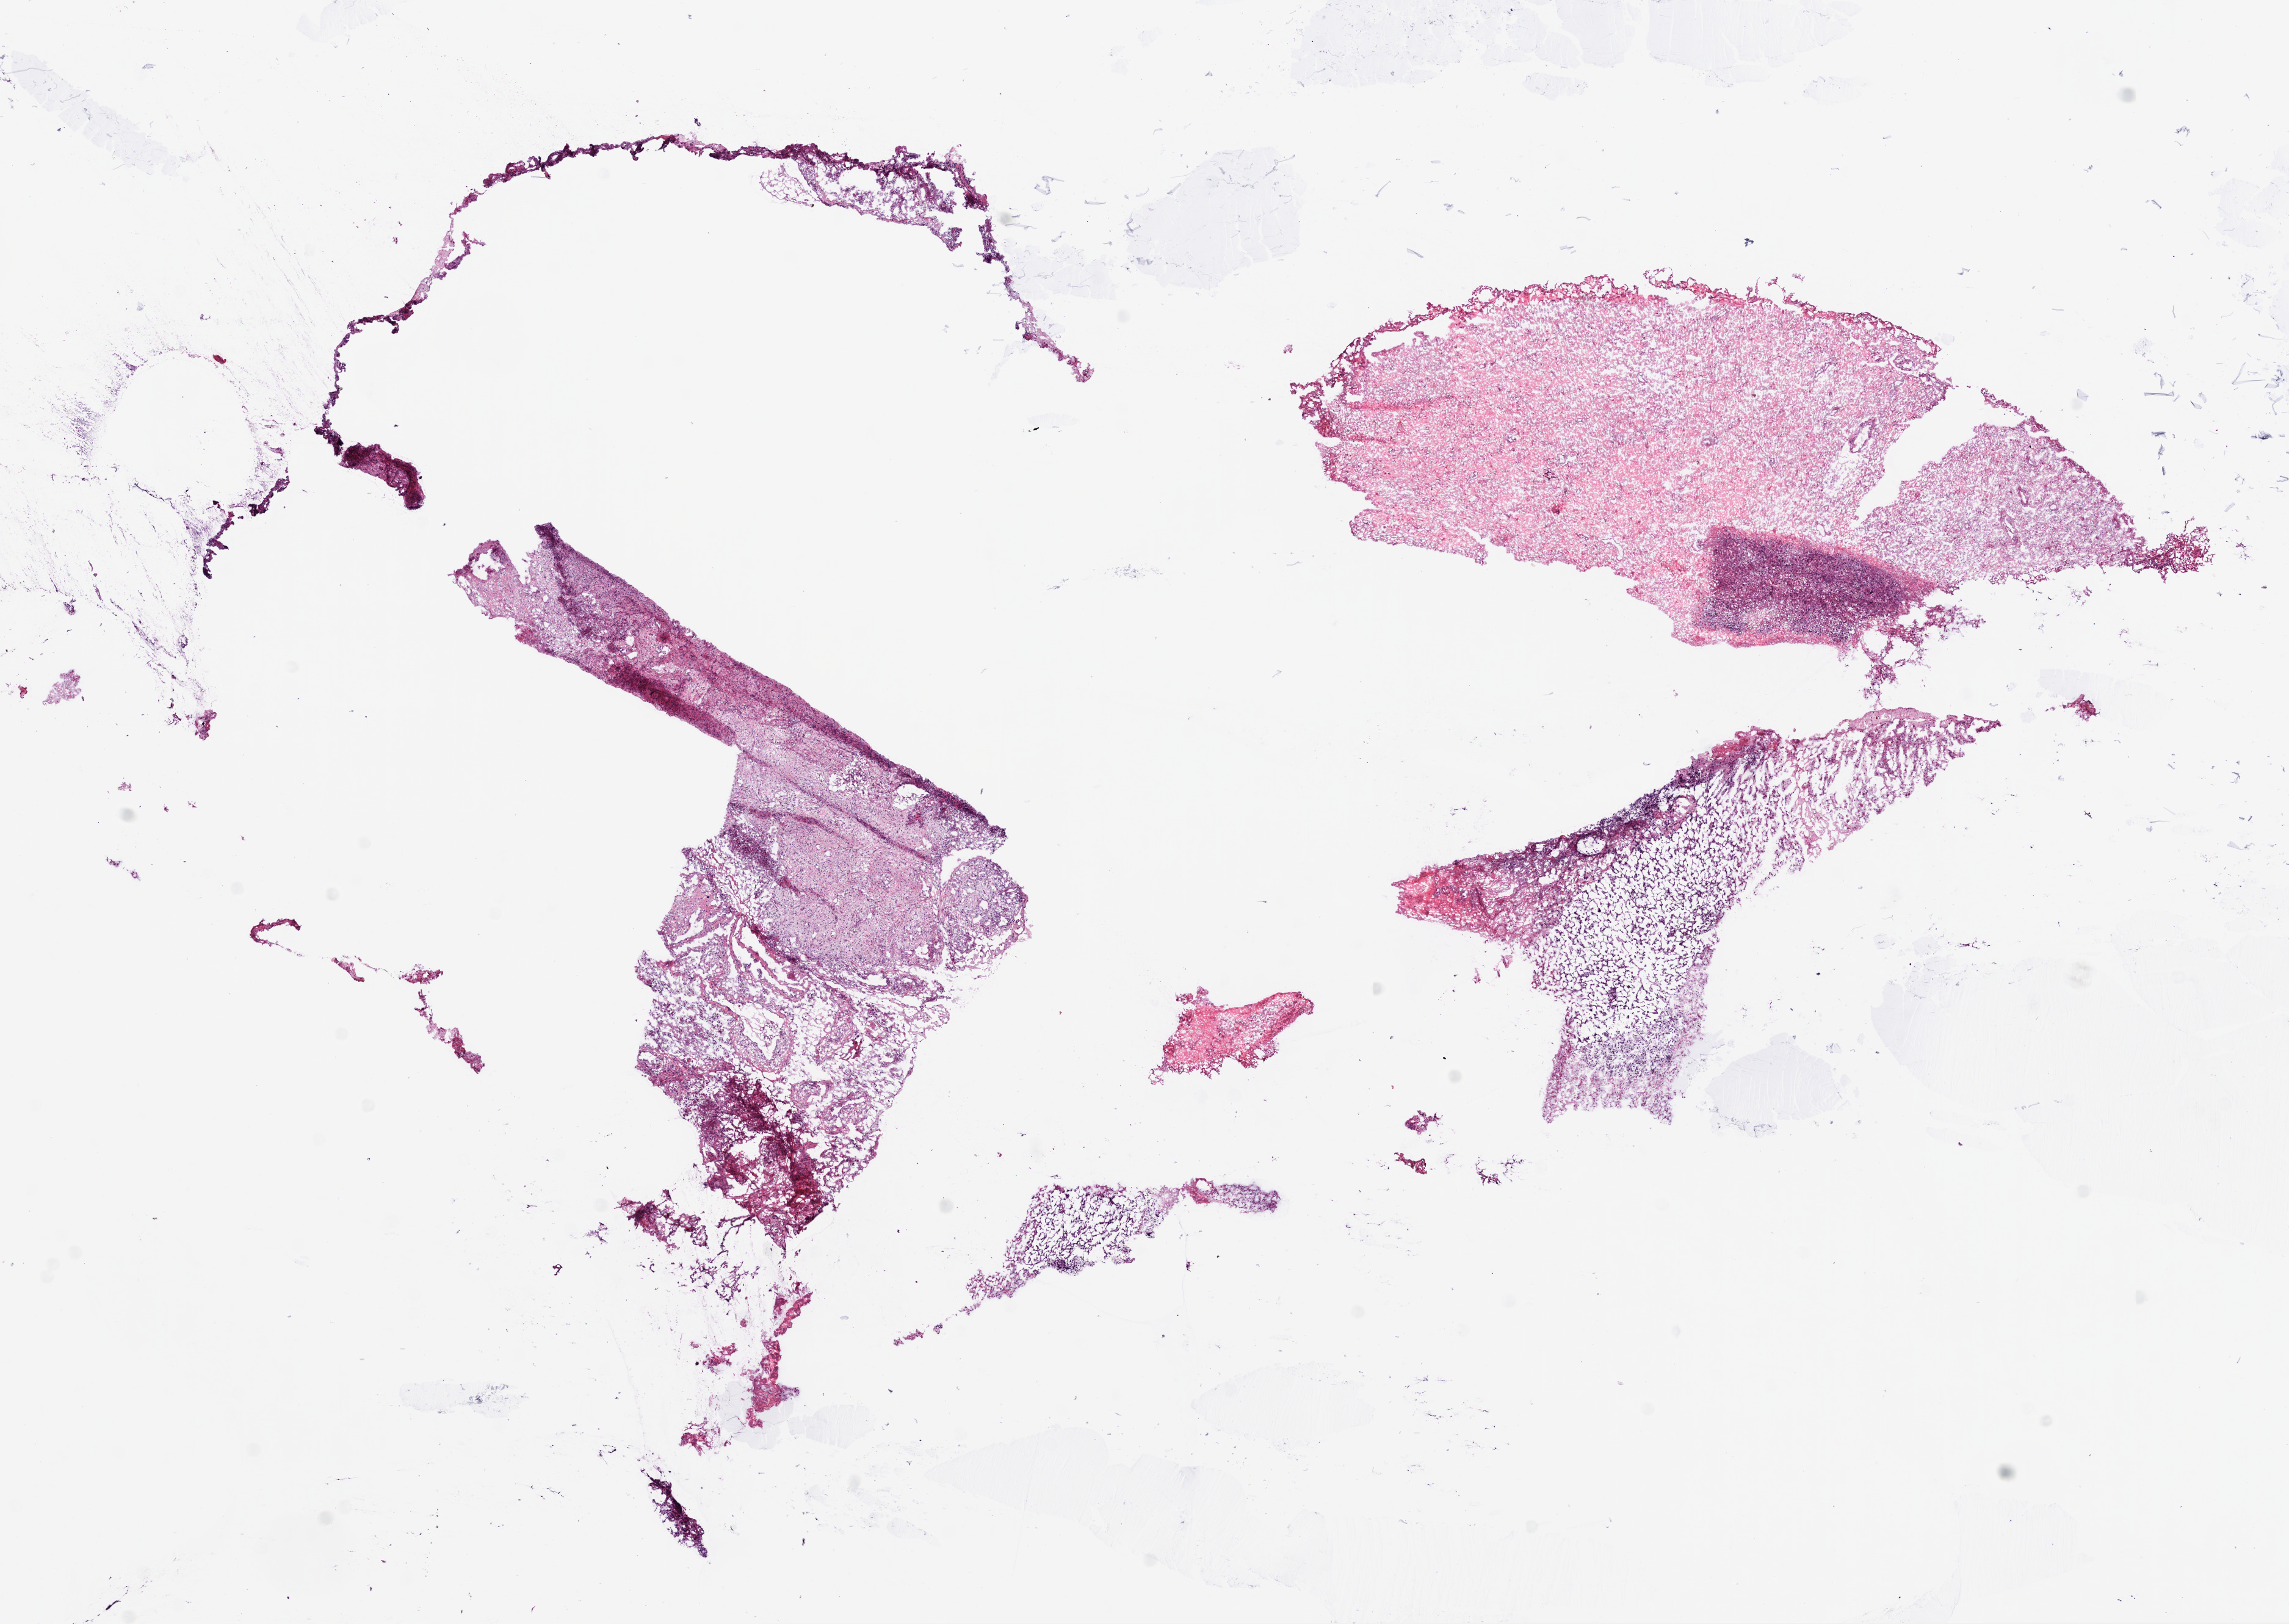
Whole-slide histology image, Hematoxylin and eosin (H&E) stained — low-resolution overview of the scanned area, about 15.0 x 10.7 mm (from a 20x scan). Frozen section from the bottom of the tissue portion. Sample: primary tumour, brain. Male patient; age at initial diagnosis 74 years. Pathologist review of this section (percent, as recorded): tumour cells 82%, tumour nuclei 70%, normal cells 0%, stromal cells 10%, necrosis 2%.
Diagnosis: Glioblastoma.